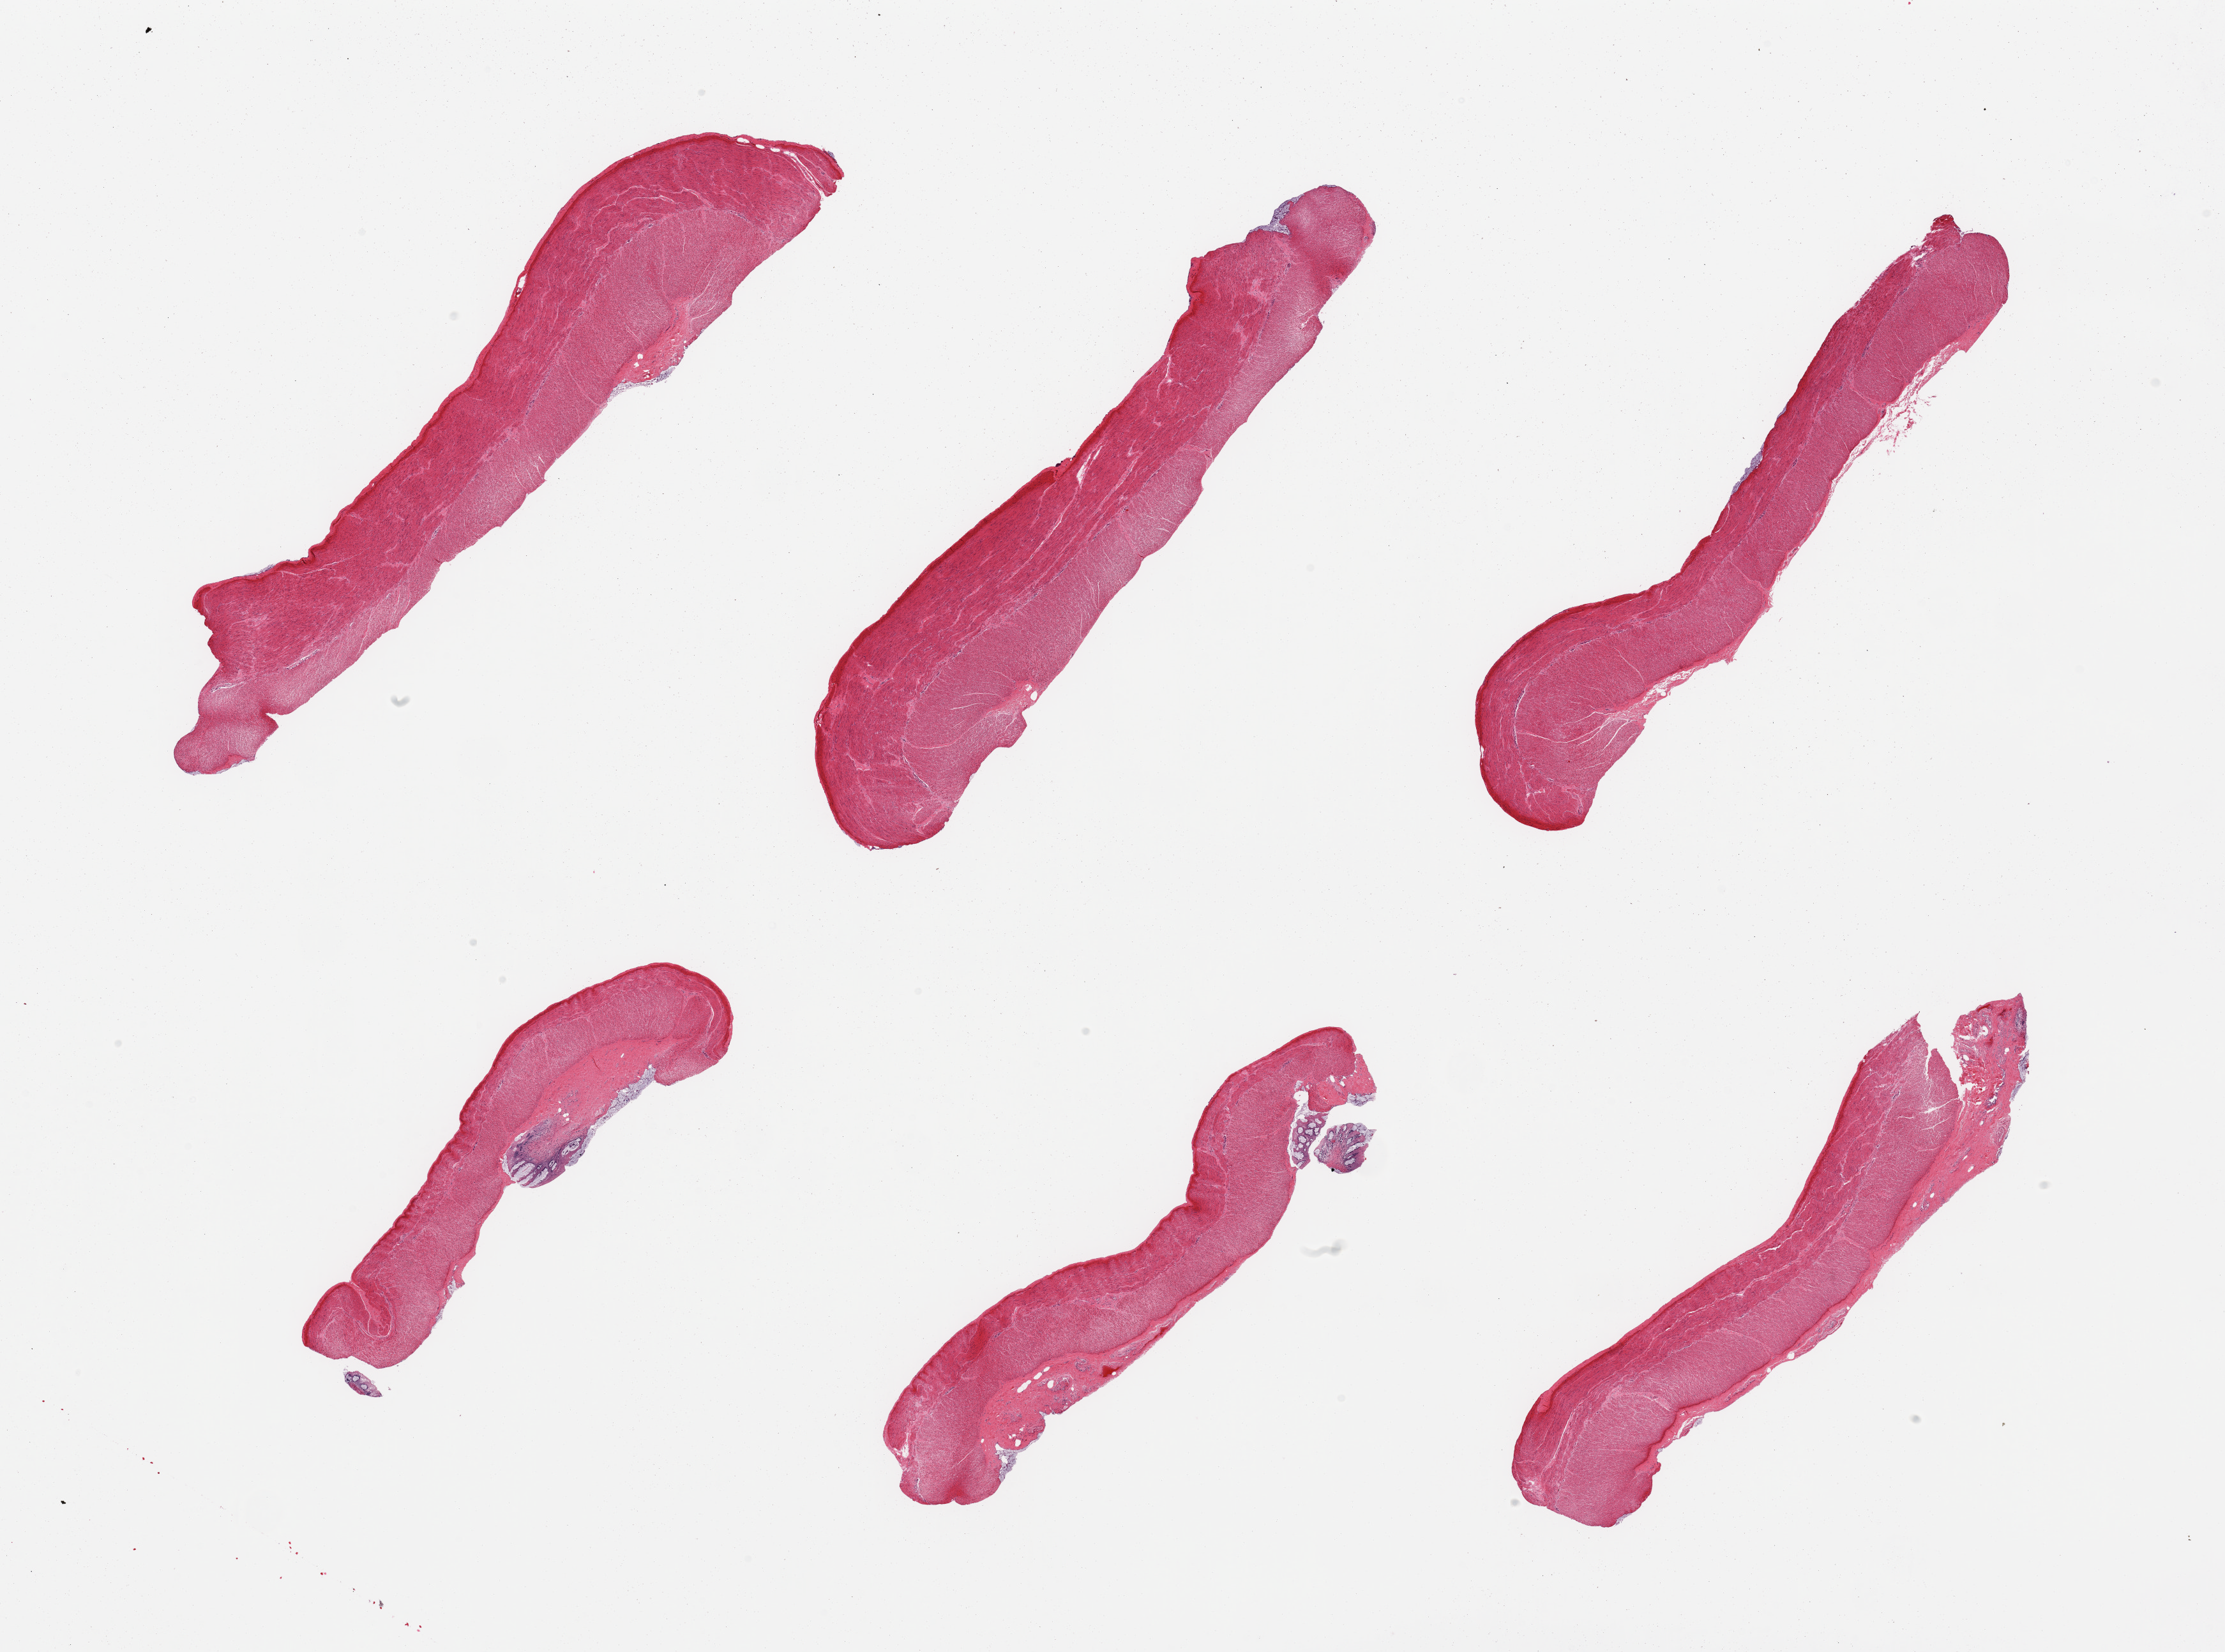
H&E whole-slide image, brightfield, whole scanned area (about 27.6 x 20.5 mm, from a 20x scan) shown as a low-resolution overview; PAXgene-fixed paraffin-embedded (PFPE) section; sampled site (target tissue): sigmoid colon; donor tissue sample. Donor sex: male.
Pathologist's review note for this sample: 6 pieces; remnants of mucosa on 2 pieces.